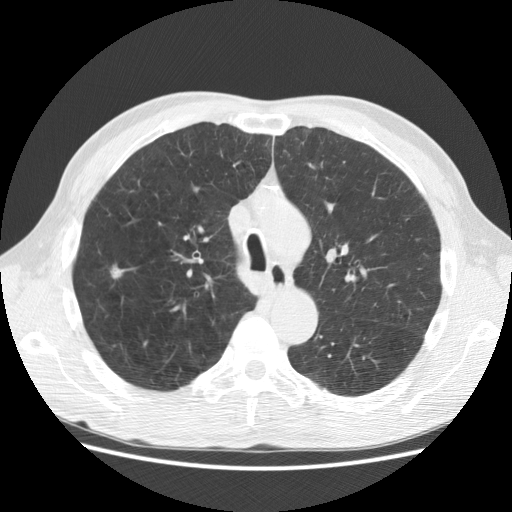
Axial slice from a low-dose chest CT screening exam. First (baseline) screen. Lung window (W 1500 / L -600 HU). Standard (soft-tissue) reconstruction kernel (STANDARD). 120 kVp. Slice 79 of 282 in the series. 512 × 512 image matrix. Male participant, aged 62 years at enrolment. Current smoker at enrolment.
- Expert-annotated lung lesion, bounding box [x1, y1, x2, y2] px = [102, 260, 135, 292].
- The screening reader recorded 2 non-calcified nodules or masses ≥4 mm on this exam (right upper lobe, left lower lobe); which of them this box marks is not recorded.
- Later outcome: lung cancer diagnosed 183 days after this screen — bronchiolo-alveolar adenocarcinoma, NOS, right upper lobe, moderately differentiated (G2), stage IIA (AJCC 6th edition), 11 mm at pathology.